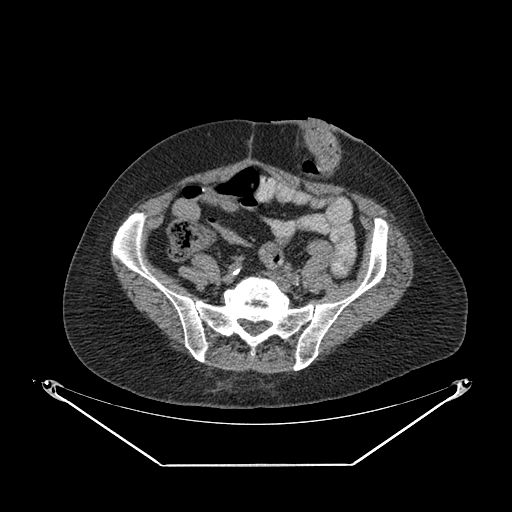
CT of an extremity soft-tissue mass (from a PET/CT study), one axial slice. Position 80 of 267 along the scan axis. 140 kVp. Soft-tissue window (W 400 / L 40 HU). 3.75 mm slice thickness. 512 × 512 image matrix, field of view 500 × 500 mm. Female patient. From the clinical record (not read from this slice): histological type: spindle cell suggestive of myxofibrosarcoma; grade: intermediate; site of the primary tumour: right buttock.
Structures marked on this image (expert contour drawn on MRI and transferred to this co-registered scan by the dataset authors):
- gross tumour volume (mass): bounding box <183,351,241,391> (left, top, right, bottom; pixels)